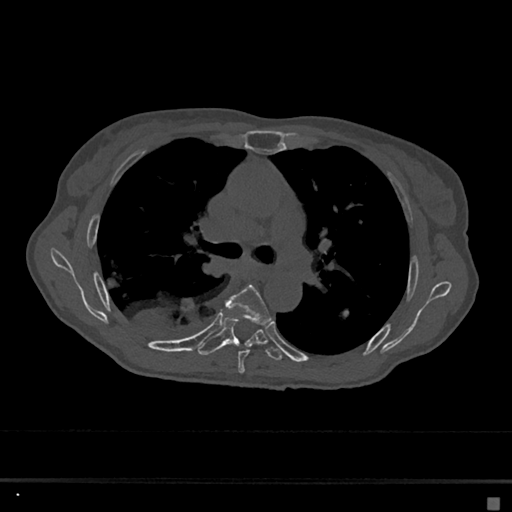
CT including the spine, one axial slice; slice 440 of 797 in the series (ordered by position); reconstruction kernel Br40s/3; bone window (W 1800 / L 400 HU); 0.5 mm slice thickness; 512 × 512 image matrix, field of view 360 × 360 mm. Female patient, age 68 years. From the clinical record (not read from this slice): primary cancer: renal.
Structures marked on this image (semi-automatic segmentation, software-assisted and operator-edited):
- T5 vertebra: bounding box (x1, y1, x2, y2) in pixels: (226, 285, 271, 374)
- T6 vertebra: (197, 317, 282, 361)